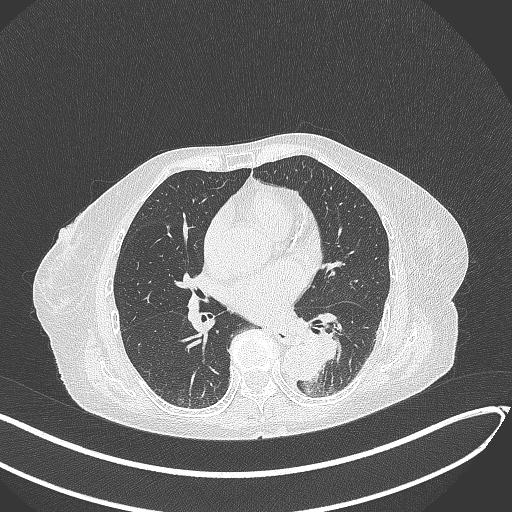
Chest CT, one axial slice; position 119 of 324 along the scan axis; lung window (W 1500 / L -600 HU); 1 mm slice thickness; 512 × 512 image matrix. Female patient, age 82 years. Case-level facts recorded for this patient, not image findings: clinical TNM (as recorded): T1b N0 M1.
Annotated regions visible in this slice (rectangle marked by the reading radiologist):
- lung tumour (recorded histology: adenocarcinoma): bounding box [x1, y1, x2, y2] px = [299, 325, 347, 368]